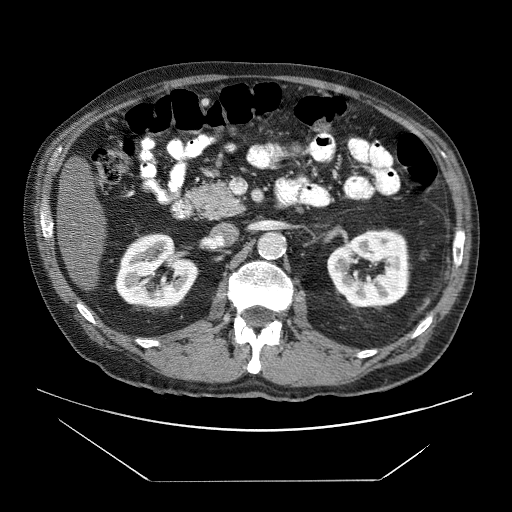
Contrast-enhanced abdominal CT (liver protocol), one axial slice; slice 16 of 83 in the series (ordered by position); reconstruction kernel STANDARD; 120 kVp; soft-tissue window (W 400 / L 40 HU); 2.5 mm slice thickness; 512 × 512 image matrix, field of view 420 × 420 mm. Case-level facts recorded for this patient, not image findings: diagnosis: hepatocellular carcinoma (patient treated with transarterial chemoembolisation; whether this scan precedes or follows treatment is not stated here); TNM stage (as recorded): Stage-IVB; Child-Pugh class: B; tumour nodularity: uninodular.
Structures marked on this image (semi-automatic segmentation, software-assisted and operator-edited):
- liver parenchyma outside the tumour (the mass and vessels are separate outlines, so this box may not span the whole liver): bounding box (x1, y1, x2, y2) in pixels: (57, 195, 106, 290)